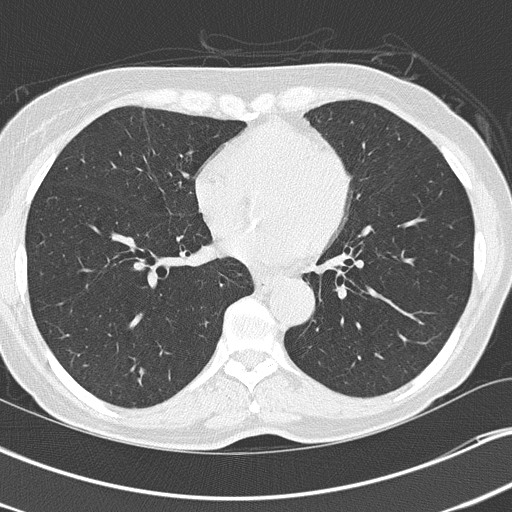
Low-dose screening chest CT, axial slice, second screening round (one year after baseline), lung window (W 1500 / L -600 HU), 2 mm slice thickness, lung (sharp) reconstruction kernel (B50f), 120 kVp, 512 × 512 image matrix, field of view 320 × 320 mm. Female, age 67 years at enrolment. Current smoker at enrolment.
Expert reader's lesion annotation, bounding box (x1, y1, x2, y2) in pixels: (130, 360, 163, 387). The screening reader recorded 2 non-calcified nodules or masses ≥4 mm on this exam; which of them this box marks is not recorded. Later outcome: lung cancer diagnosed 507 days after this screen (after the third annual screen) — adenocarcinoma, NOS, left lower lobe, poorly differentiated (G3), stage IA (AJCC 6th edition), 25 mm at pathology.